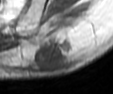
MRI of an extremity soft-tissue mass, one axial slice. Position 15 of 42 along the scan axis. MR volume resampled by the dataset authors to the PET/CT grid (not the native acquisition matrix). 113 × 94 image matrix. Male patient. From the clinical record (not read from this slice): histological type: leiomyosarcoma; grade: intermediate; site of the primary tumour: left pelvis.
Outlined on this slice (expert contour drawn on MRI and transferred to this co-registered scan by the dataset authors):
- gross tumour volume (mass): box from (x=35, y=39) to (x=73, y=72) px